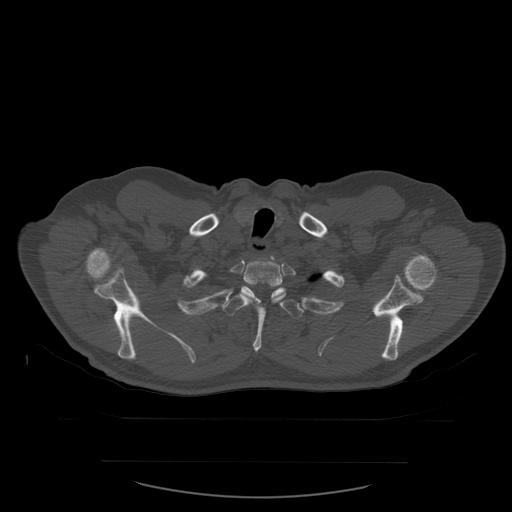
CT including the spine, one axial slice; slice 468 of 590 in the series (ordered by position); bone window (W 1800 / L 400 HU); 512 × 512 image matrix, field of view 479 × 479 mm. Patient age 71 years. From the clinical record (not read from this slice): primary cancer: lung.
Annotated regions visible in this slice (semi-automatically segmented with operator editing):
- T1 vertebra: bounding box (x1, y1, x2, y2) in pixels: (259, 257, 274, 260)
- T2 vertebra: (241, 257, 285, 303)
- T3 vertebra: (222, 288, 304, 353)